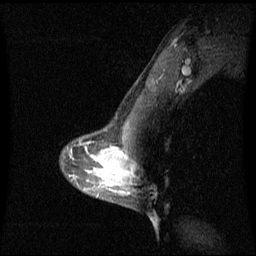
Breast MRI (dynamic contrast-enhanced), one sagittal slice. Slice 45 of 60 in the series (ordered by position). Dynamic contrast-enhanced series, image 2 of 3 at this slice position (ordered by acquisition). 1.5 T. TE 4.2 ms, TR 8.4 ms. 2.3 mm slice thickness. 256 × 256 image matrix, field of view 240 × 240 mm. Female patient, age 42 years. From the clinical record (not read from this slice): setting: breast cancer imaged before/during neoadjuvant chemotherapy; receptor status: triple-negative.
Outlined on this slice (semi-automatically segmented with operator editing):
- analysis volume of interest (the breast-tissue region the enhancement analysis was run in; not a lesion): bounding box (x1, y1, x2, y2) in pixels: (106, 156, 131, 195)
- tumour enhancement mask (voxels above the 70 % enhancement threshold inside the analysis volume of interest): (124, 172, 129, 177)